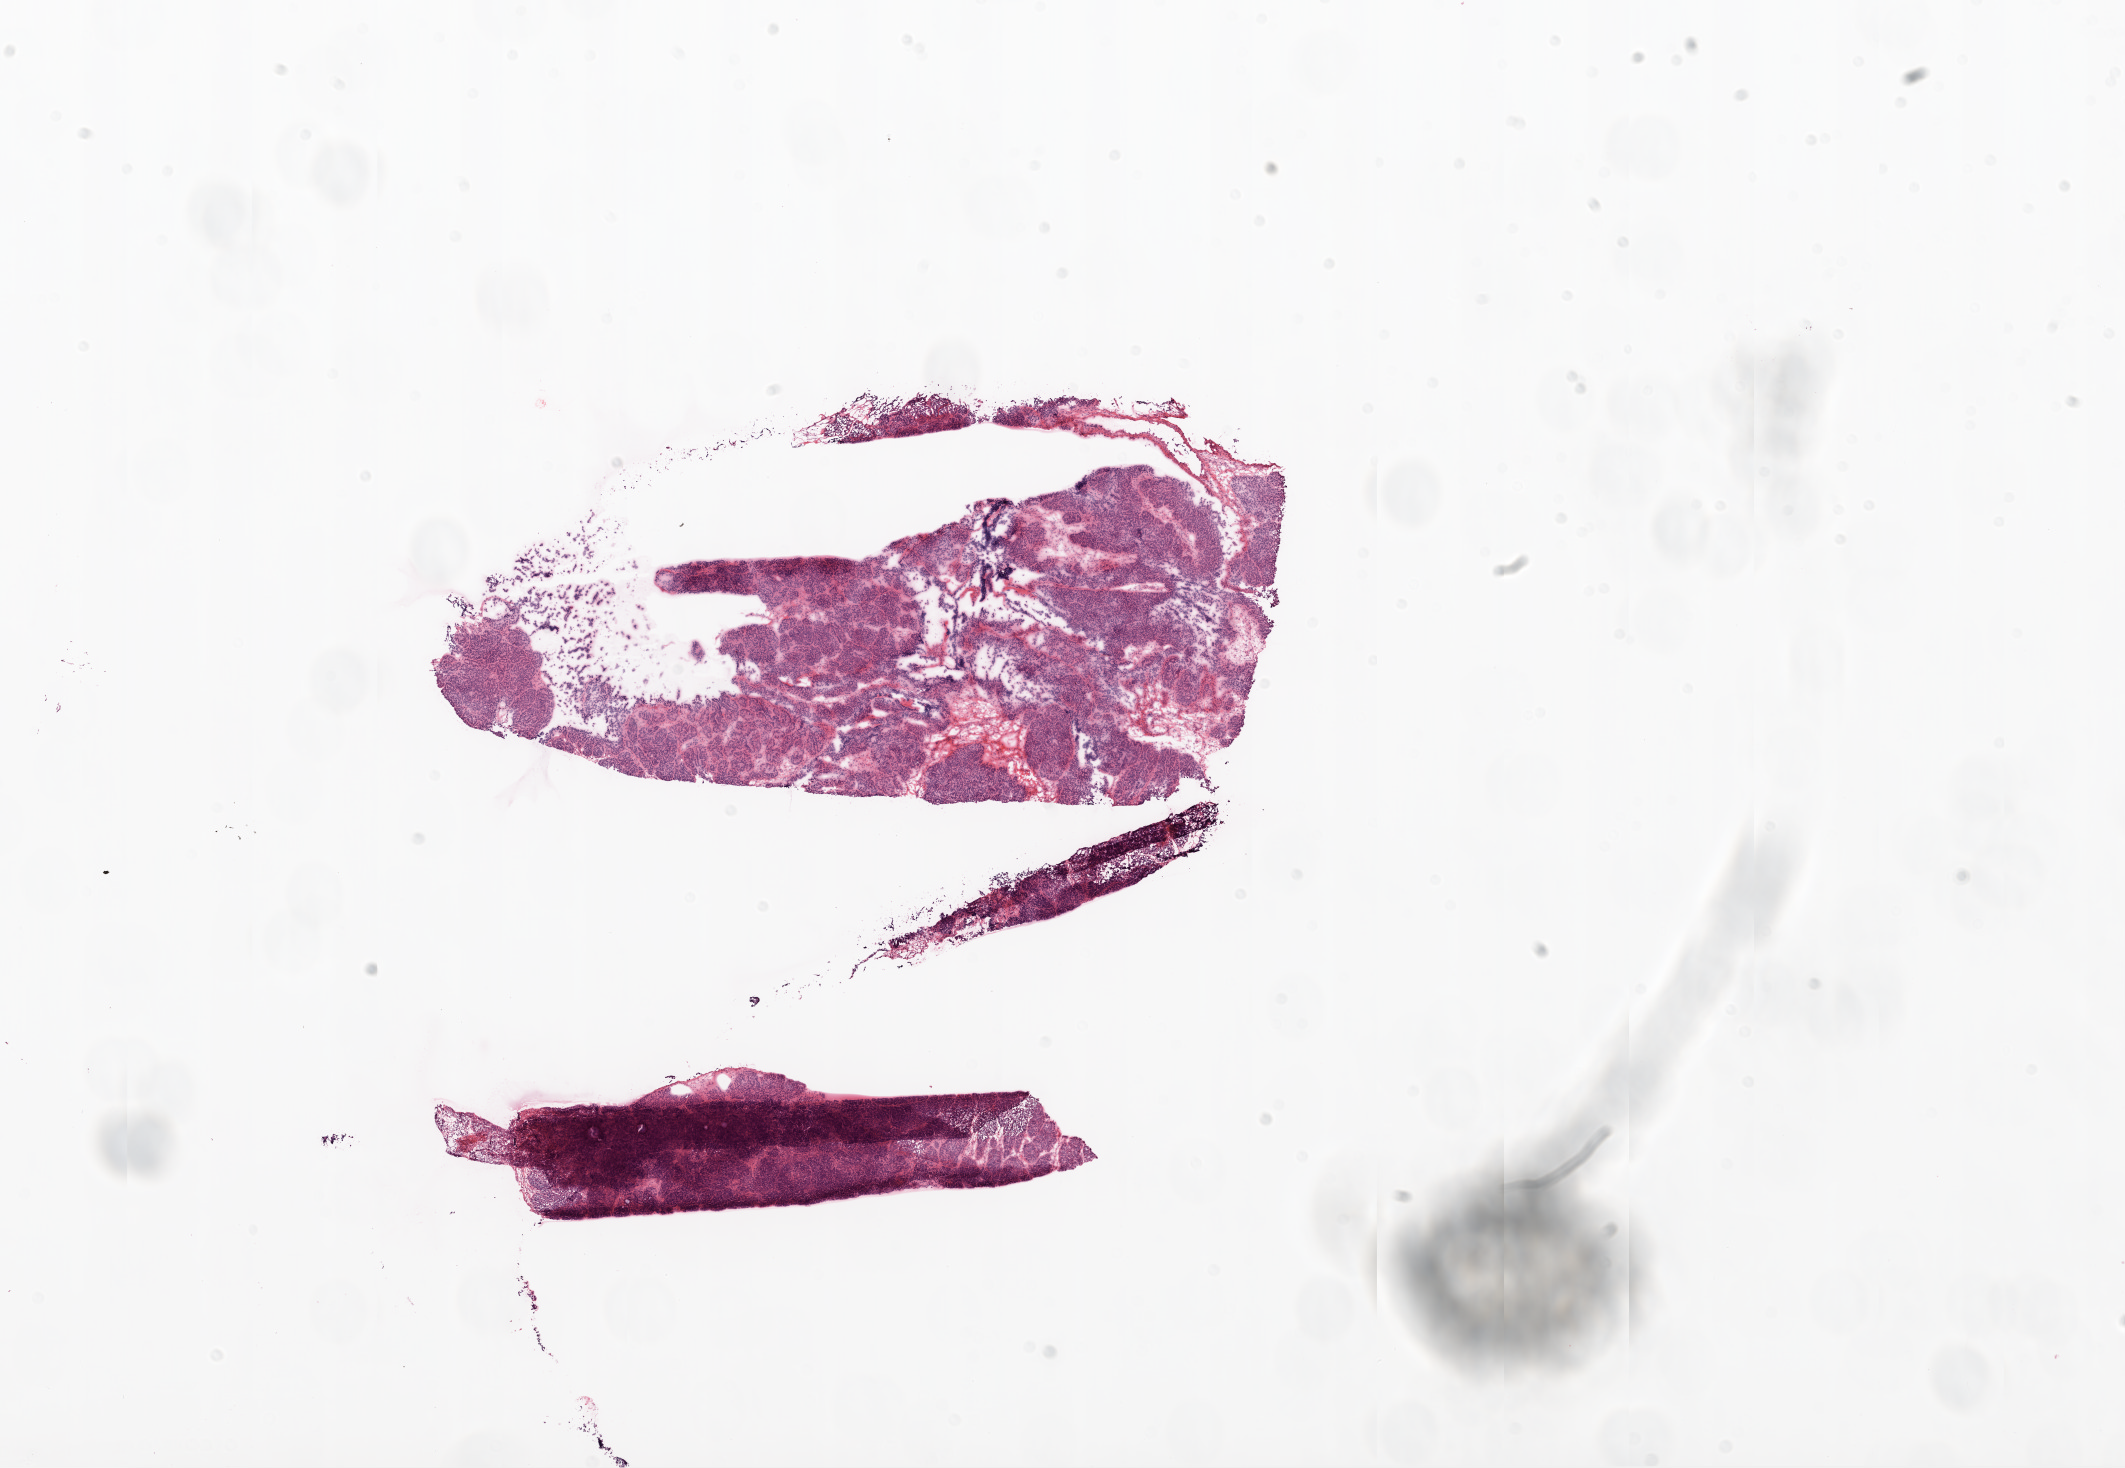
H&E whole-slide image — a low-resolution overview of the entire scanned area, about 17.1 x 11.8 mm. Frozen section from the top of the tissue portion. Ovary, primary tumour sample. Patient: female, age at initial diagnosis 59 years. Histologic grade: G3 (poorly differentiated). Composition of this section per pathologist review: tumour cells 90%, tumour nuclei 90%, normal cells 0%, stromal cells 10%, necrosis 0%. Inflammatory infiltration, as recorded: lymphocyte infiltration 0%, monocyte infiltration 0%, neutrophil infiltration 0%.
Laterality: bilateral. FIGO stage: IIIC. Pathologic diagnosis: Serous cystadenocarcinoma, NOS.